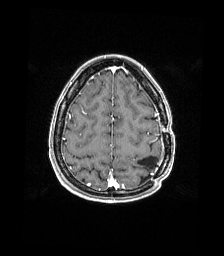
Brain MRI from a brain-tumour surgery series, one axial slice. Position 47 of 176 along the scan axis. T1-weighted post-contrast. 1 mm slice thickness. 224 × 256 image matrix. Case-level facts recorded for this patient, not image findings: histopathology: Atypical meningioma; WHO grade: 2; tumour location: Paramedian Left Parietal.
Structures marked on this image (outlined manually by an expert reader):
- previous resection cavity: bounding box (x1, y1, x2, y2) in pixels: (138, 157, 157, 169)